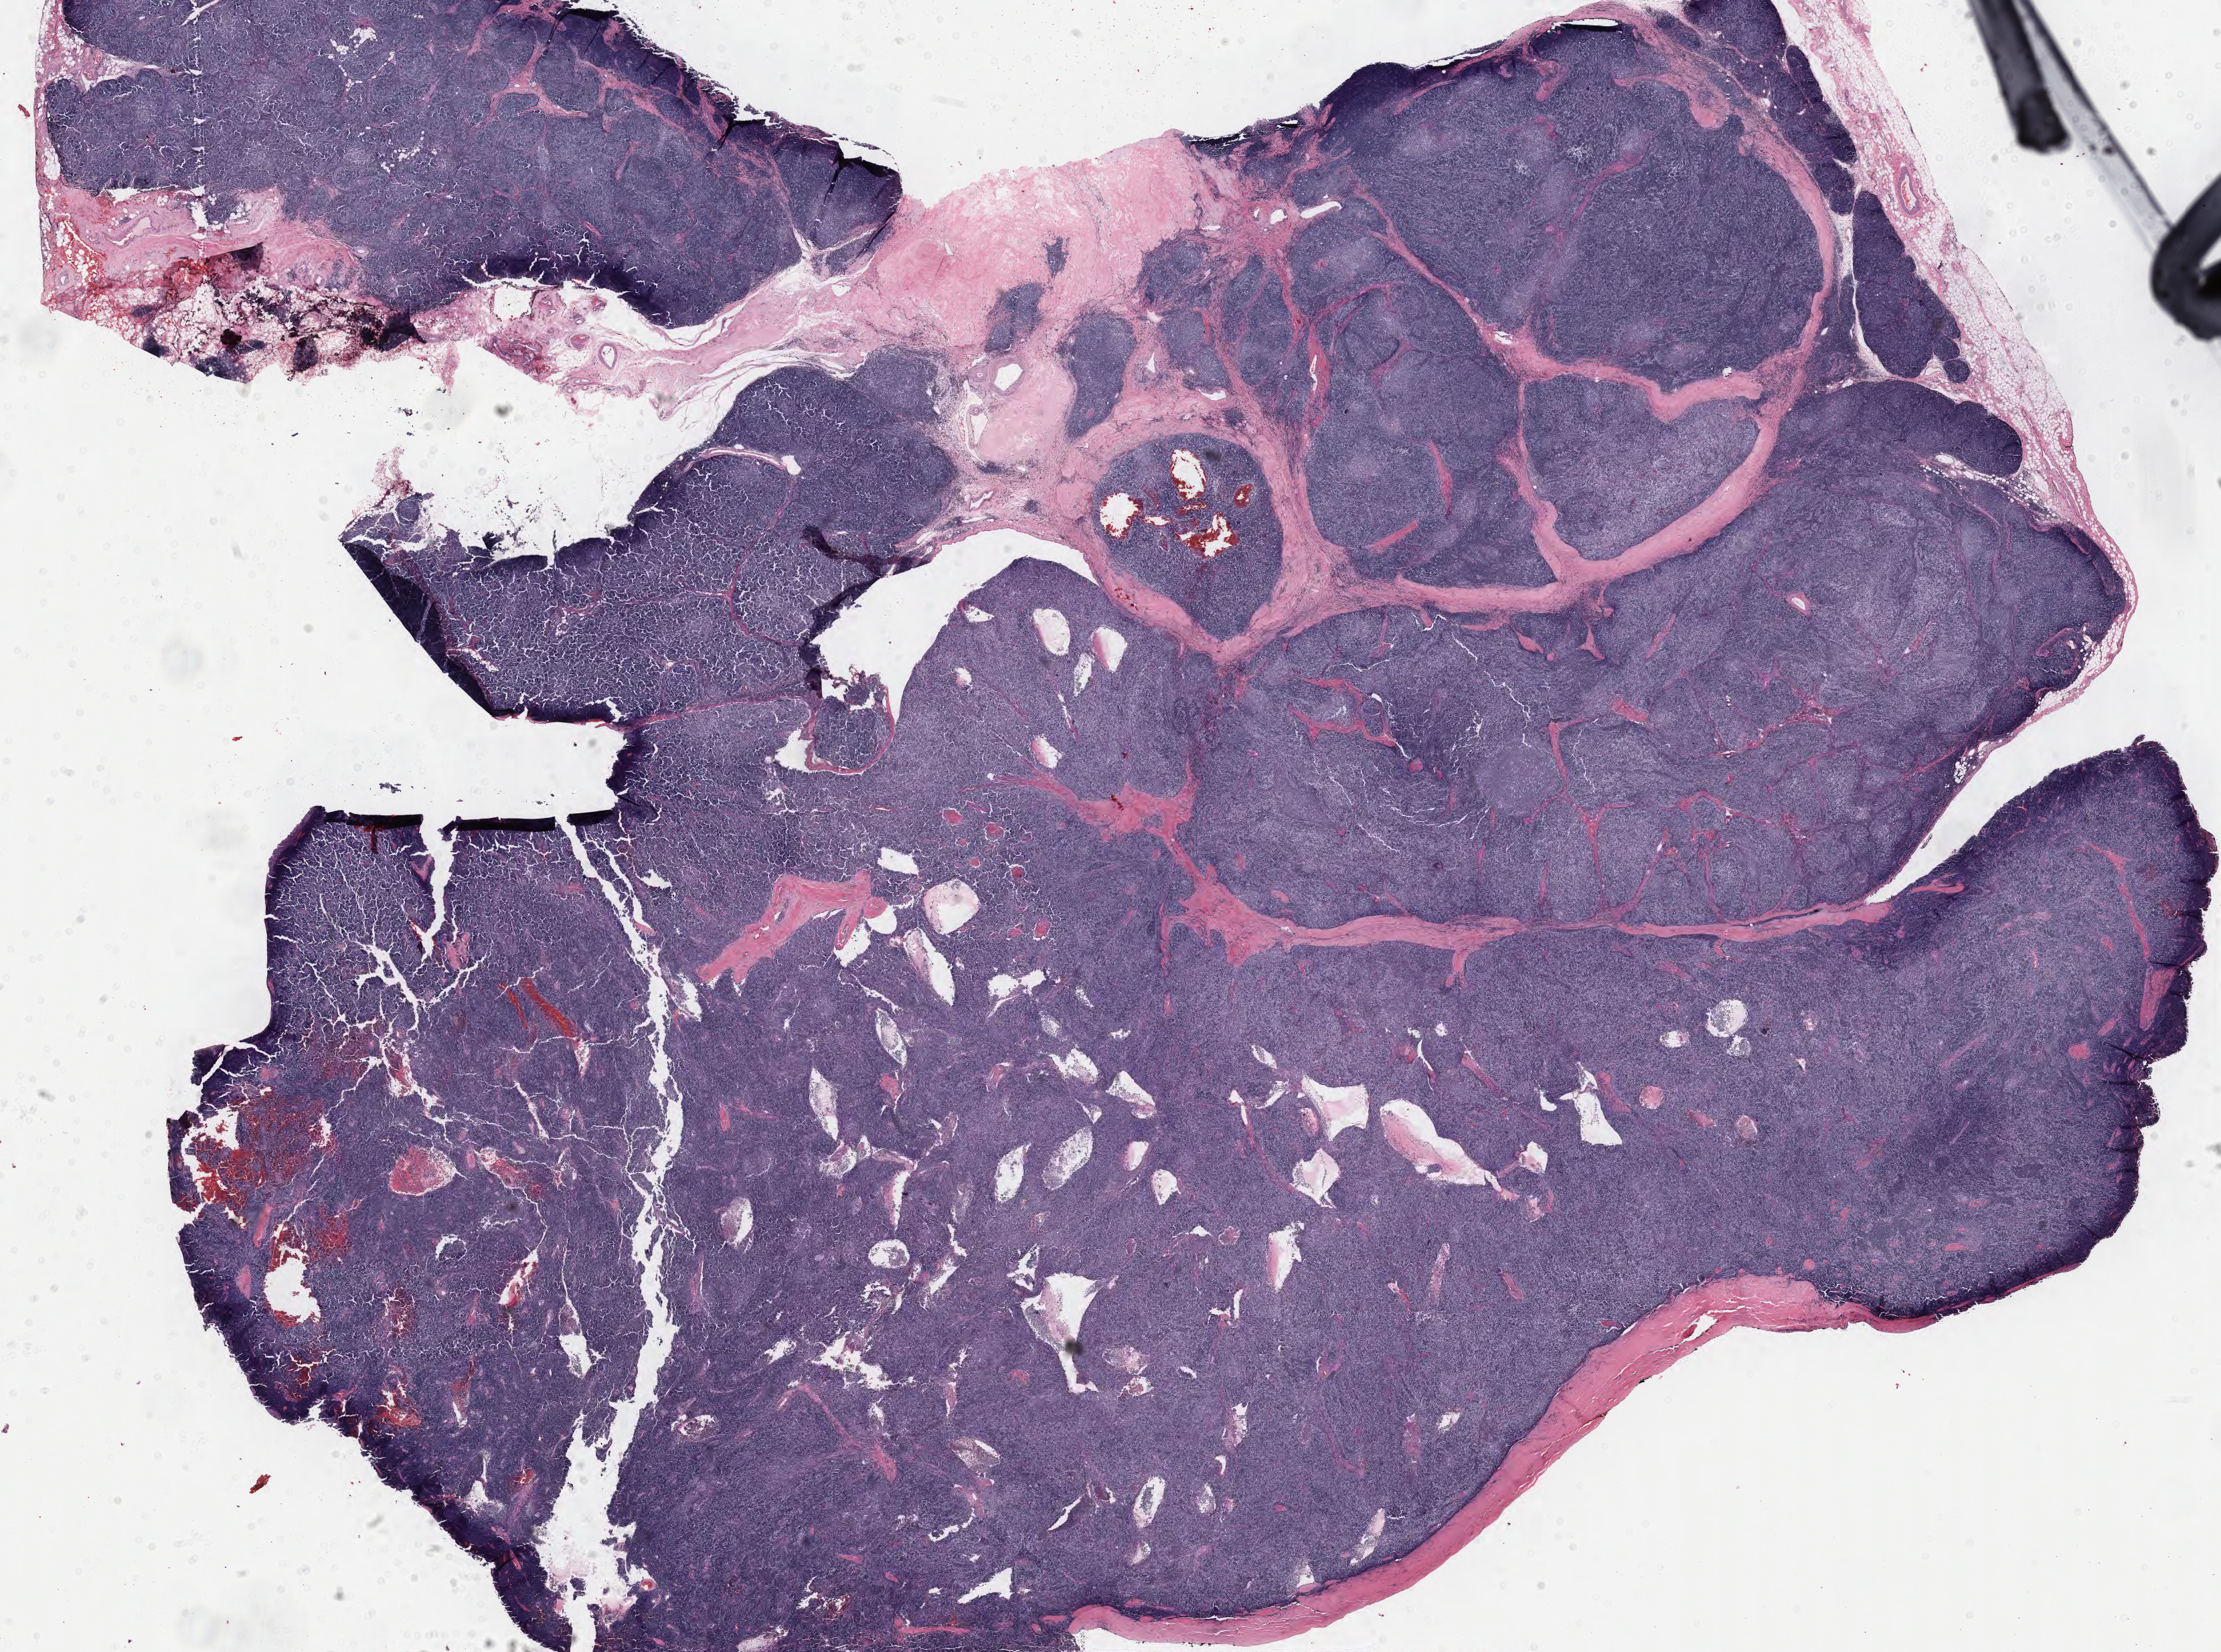
Digitized Hematoxylin and eosin (H&E) stained tissue section (whole slide), a low-resolution overview of the entire scanned area, about 26.3 x 19.6 mm (slide scanned at 40x). Formalin-fixed paraffin-embedded (FFPE) diagnostic section. Primary tumour sample from the thymus. Male, age 44 years at initial diagnosis.
Diagnosis: Thymoma, type B2, malignant.